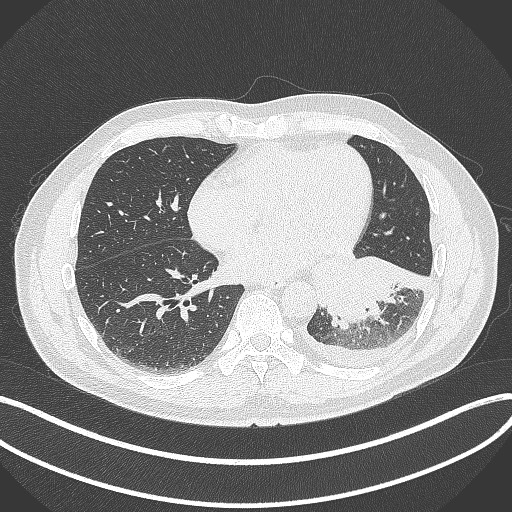
Chest CT, one axial slice. Position 138 of 342 along the scan axis. Reconstruction kernel B70f. 120 kVp. Lung window (W 1500 / L -600 HU). 1 mm slice thickness. 512 × 512 image matrix, field of view 400 × 400 mm. Male patient, age 58 years. From the clinical record (not read from this slice): clinical TNM (as recorded): T3 N1 M1b; histopathological grade: G3.
Outlined on this slice (bounding box drawn by a radiologist):
- lung tumour (recorded histology: small cell carcinoma): bounding box <305,241,426,328> (left, top, right, bottom; pixels)